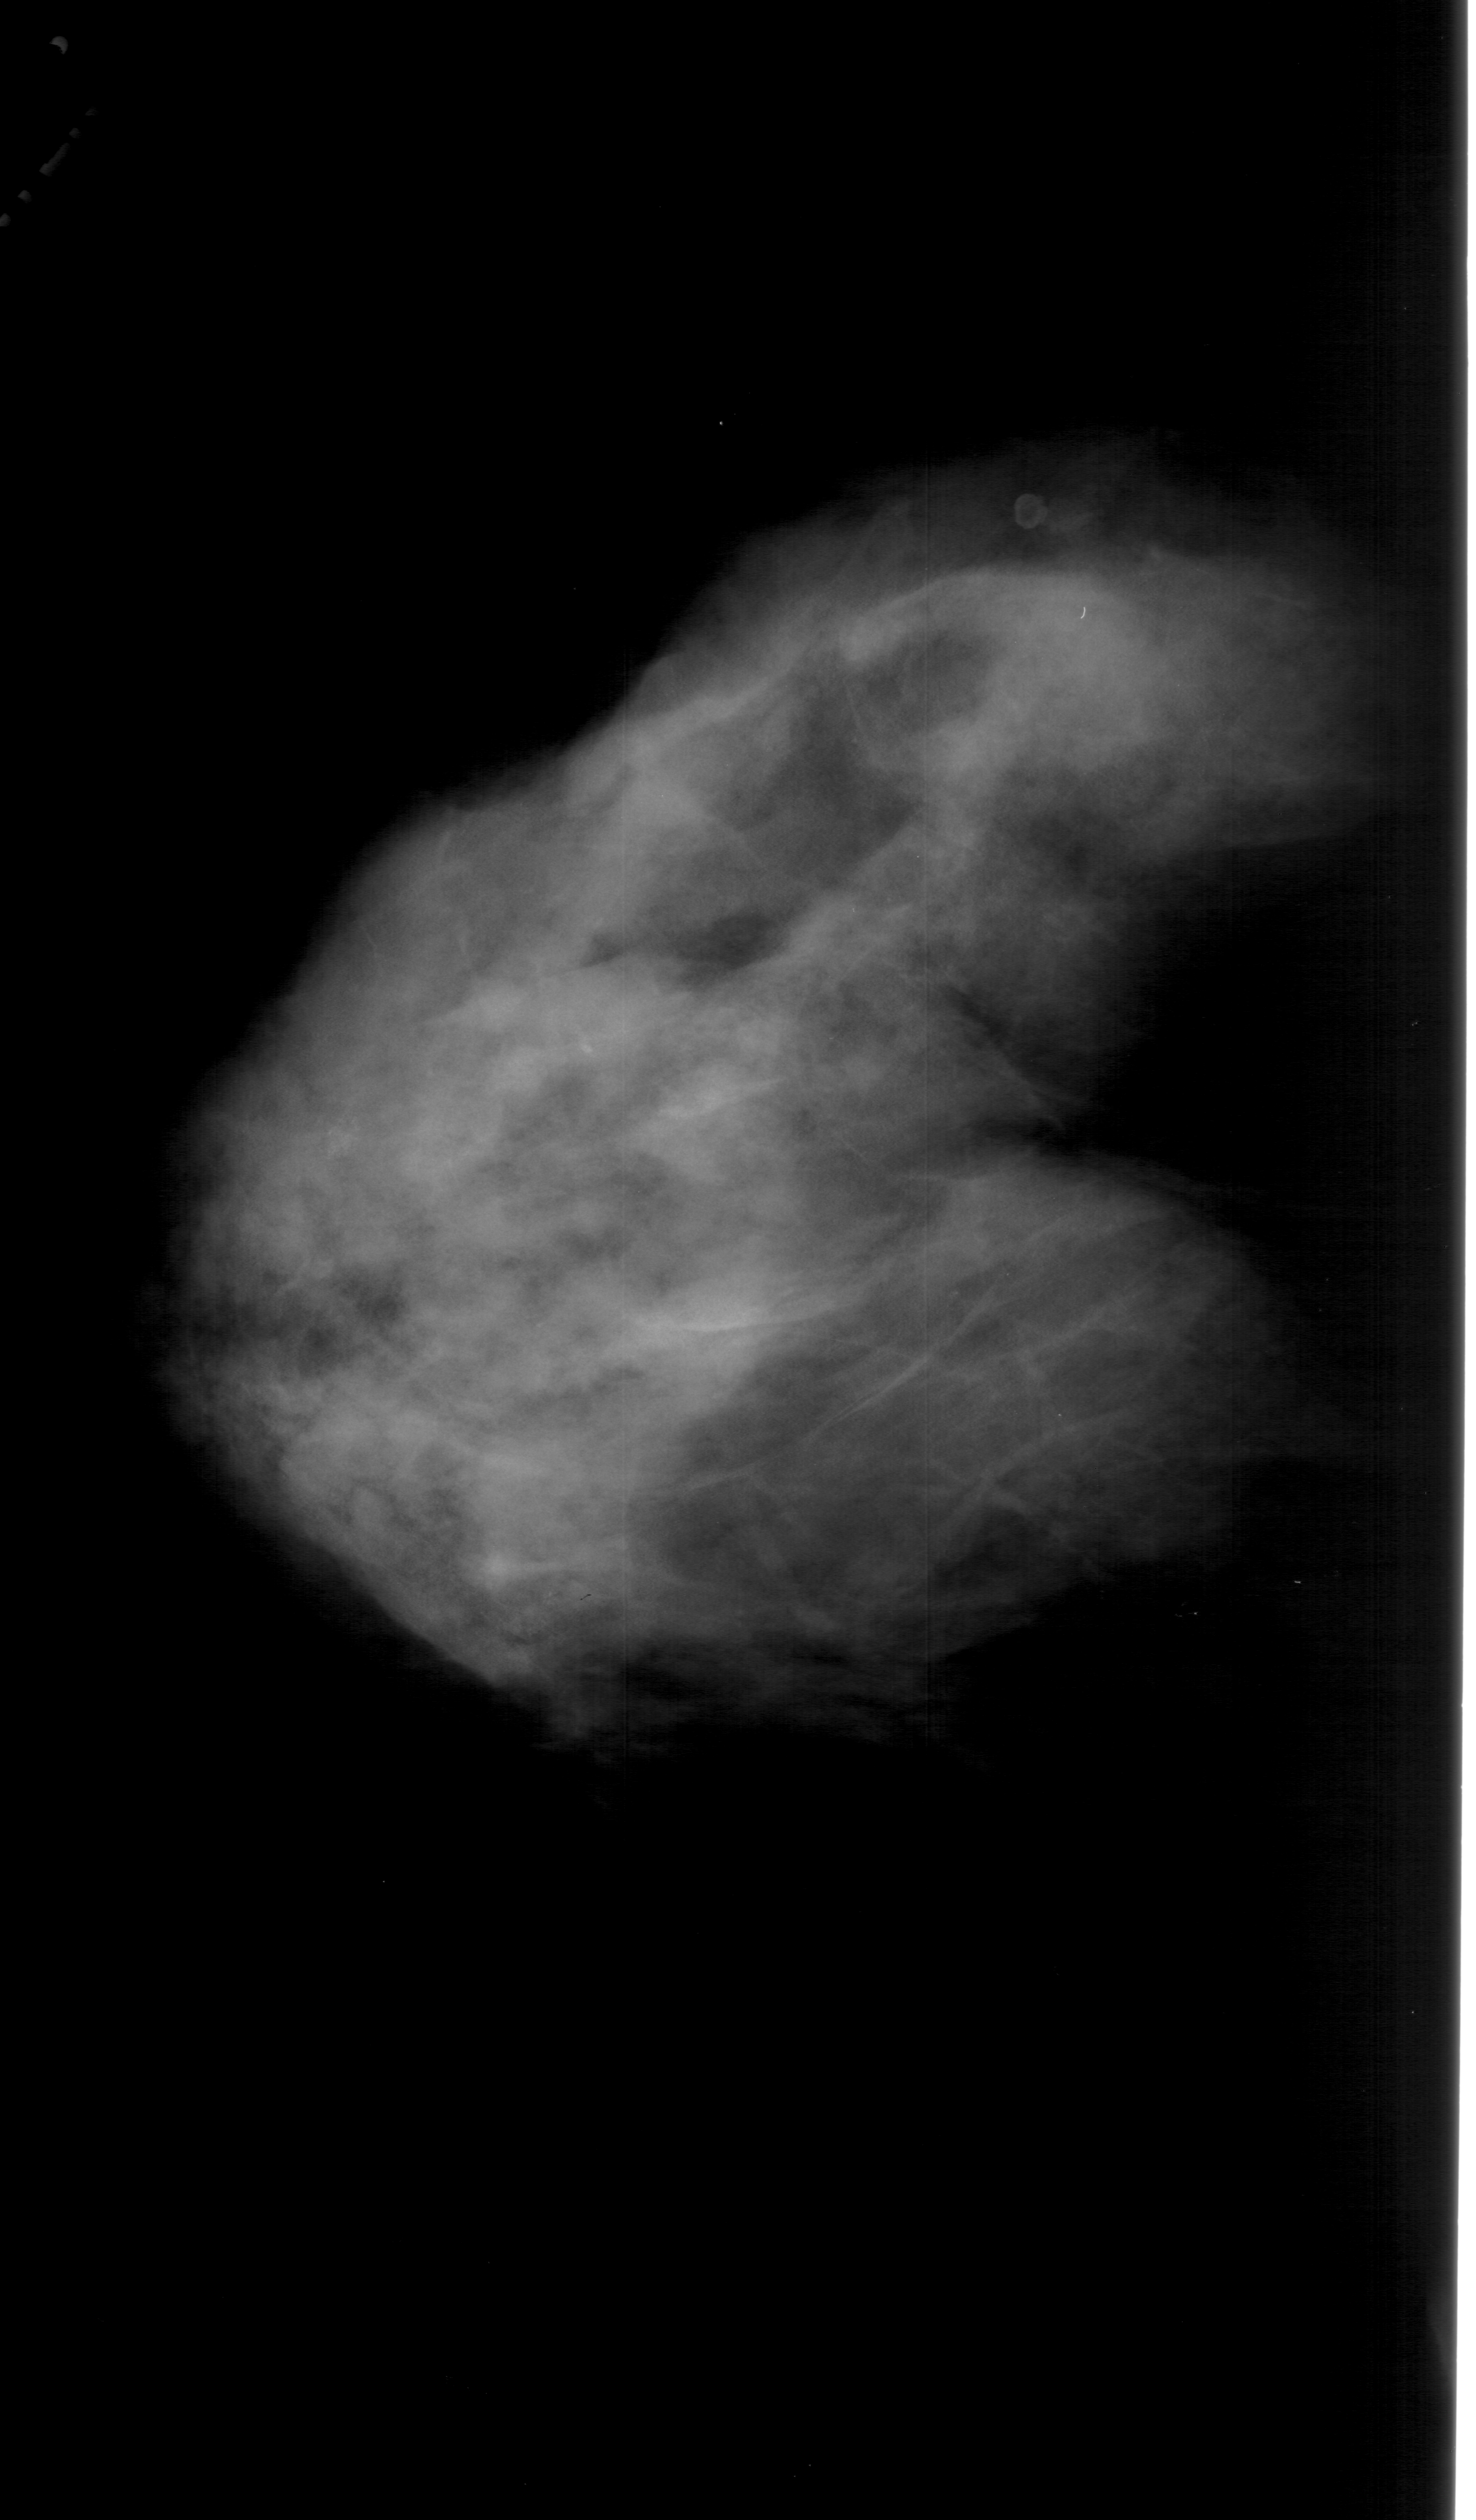
Mammogram (digitized film); left breast; CC view; breast composition: extremely dense (BI-RADS density category 4 of 4).
Calcifications, morphology pleomorphic, distribution clustered; BI-RADS assessment category 4; pathology (as recorded): malignant.